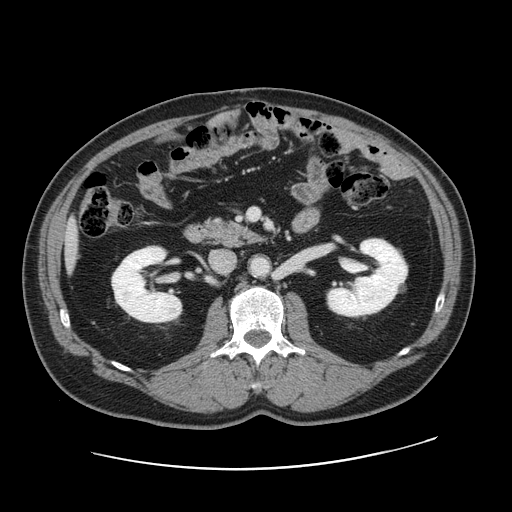
Contrast-enhanced abdominal CT, one axial slice; position 63 of 178 along the scan axis; 120 kVp; intravenous contrast given; soft-tissue window (W 400 / L 40 HU); 2.5 mm slice thickness; 512 × 512 image matrix, field of view 403 × 403 mm. Male patient, age 63 years. Case-level facts recorded for this patient, not image findings: diagnosis: colorectal cancer liver metastases, imaged before liver resection; multiple liver metastases: yes; largest metastasis: 8 cm; chemotherapy before resection: no.
Annotated regions visible in this slice (outlined manually by an expert reader):
- liver: bounding box (x1, y1, x2, y2) in pixels: (65, 226, 77, 258)